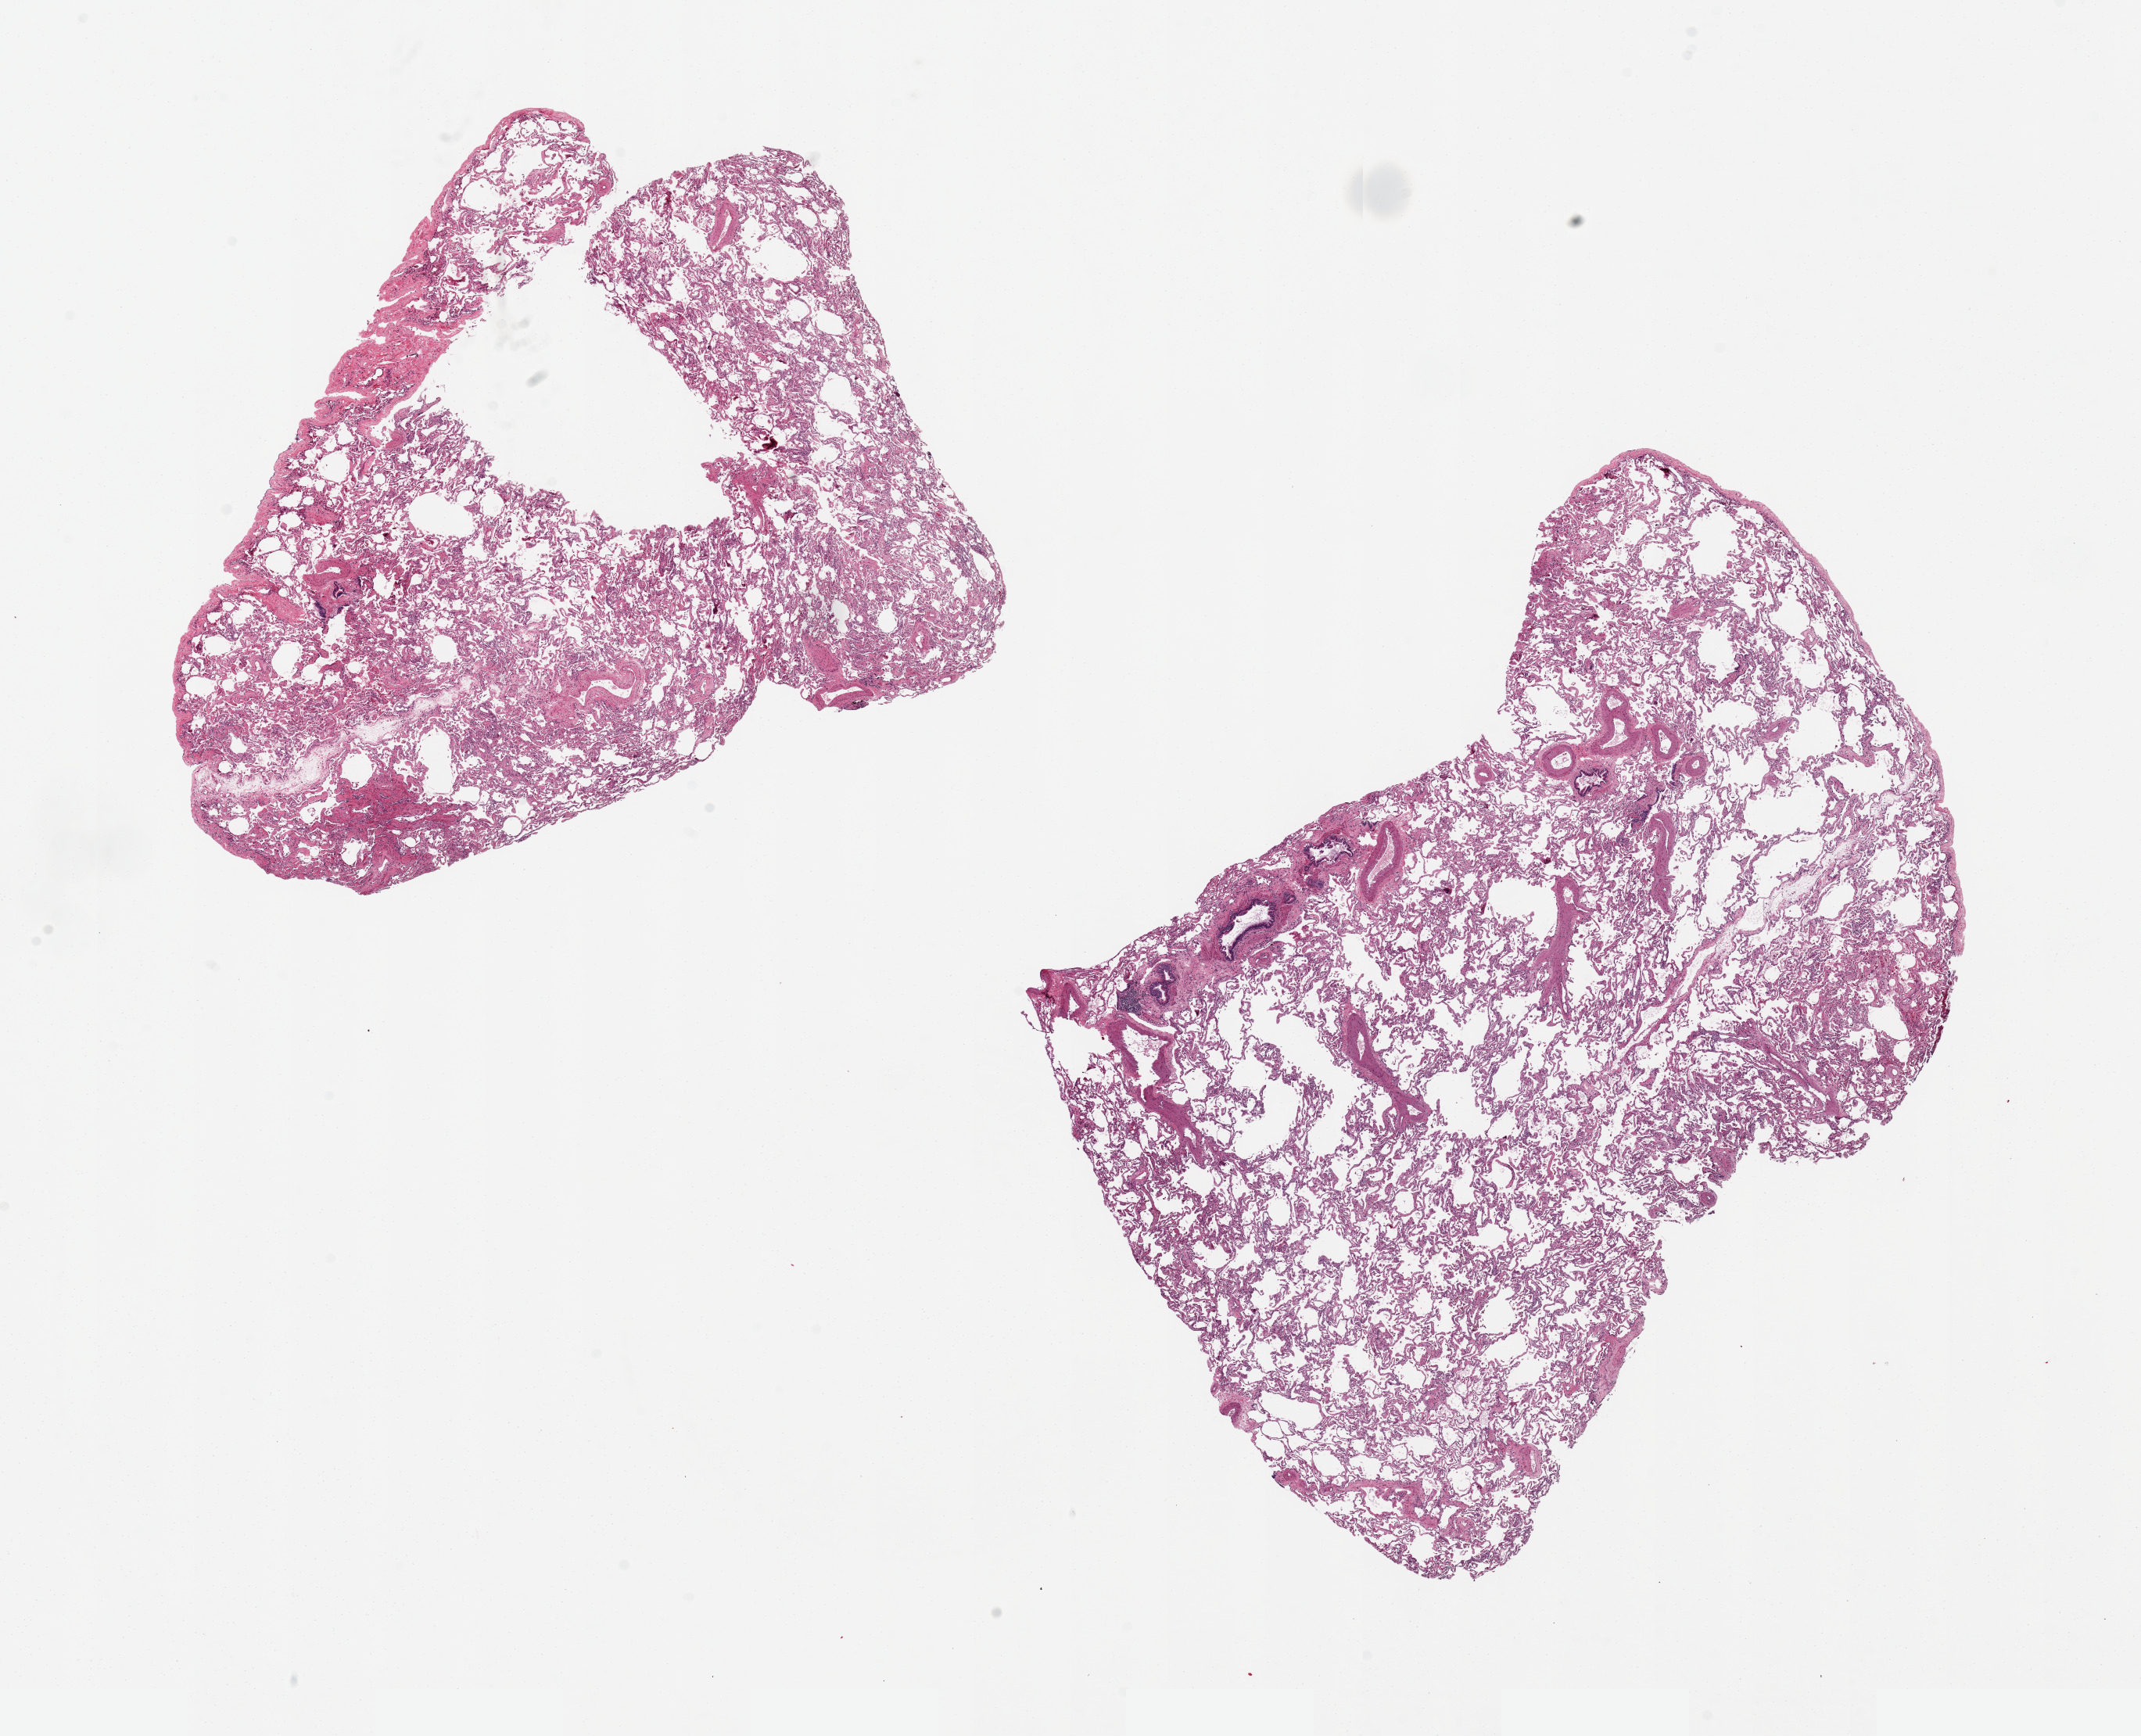
Digitized haematoxylin and eosin-stained section, brightfield, a low-resolution overview of the entire scanned area, about 21.7 x 17.6 mm, PAXgene-fixed, paraffin-embedded tissue, target tissue: lung, donor tissue sample. Donor: female.
Review note (as recorded): 2 pieces, 9x7 & 10x8mm; mild congestion.